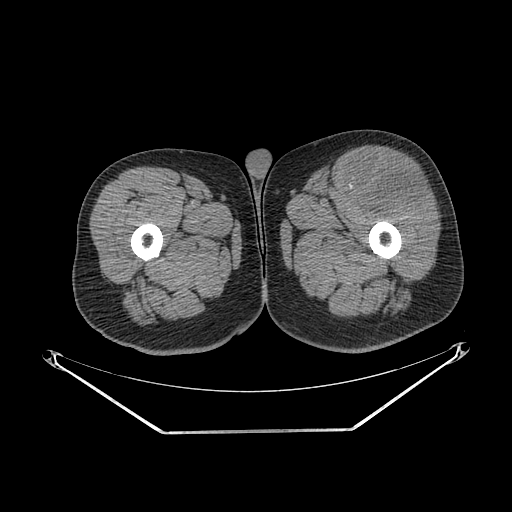
CT of an extremity soft-tissue mass (from a PET/CT study), one axial slice. Slice 245 of 267 in the series (ordered by position). Reconstruction kernel SOFT. 140 kVp. Soft-tissue window (W 400 / L 40 HU). 512 × 512 image matrix, field of view 500 × 500 mm. Male patient. Case-level facts recorded for this patient, not image findings: histological type: extraskeletal osteosarcoma; grade: high; site of the primary tumour: thigh.
Structures marked on this image (expert contour drawn on MRI and transferred to this co-registered scan by the dataset authors):
- gross tumour volume (mass): bounding box [x1, y1, x2, y2] px = [354, 162, 428, 211]